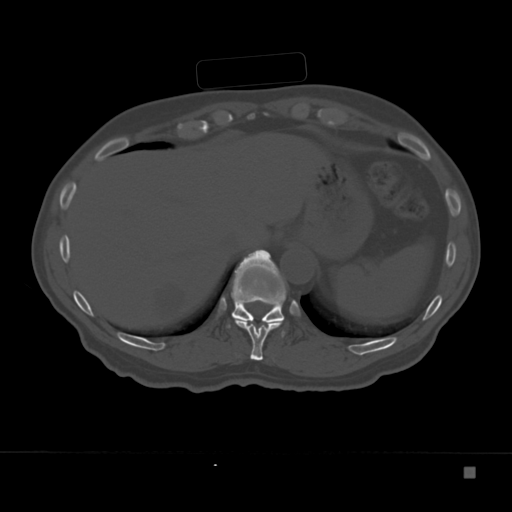
CT including the spine, one axial slice. Position 162 of 332 along the scan axis. 120 kVp. Bone window (W 1800 / L 400 HU). 1.5 mm slice thickness. 512 × 512 image matrix, field of view 389 × 389 mm. Male patient, age 72 years. From the clinical record (not read from this slice): primary cancer: skeletal.
Structures marked on this image (semi-automatically segmented with operator editing):
- T10 vertebra: box from (x=235, y=258) to (x=285, y=361) px
- T11 vertebra: (x=227, y=249)–(x=287, y=328)